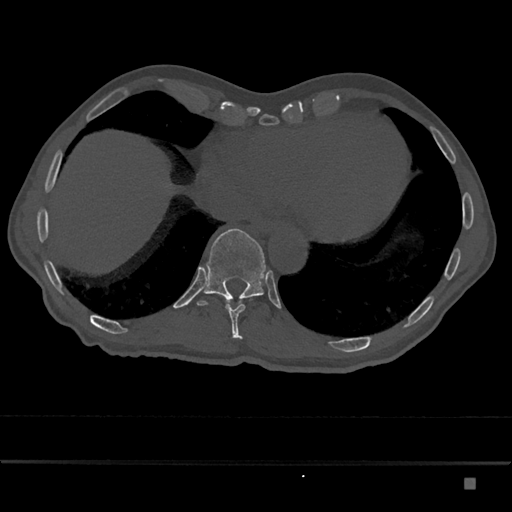
CT including the spine, one axial slice; slice 708 of 797 in the series (ordered by position); reconstruction kernel Br40s/3; bone window (W 1800 / L 400 HU); 0.5 mm slice thickness; 512 × 512 image matrix, field of view 390 × 390 mm. Male patient, age 72 years. Case-level facts recorded for this patient, not image findings: primary cancer: prostate.
Structures marked on this image (semi-automatic segmentation, software-assisted and operator-edited):
- T10 vertebra: bounding box <226,296,252,339> (left, top, right, bottom; pixels)
- T11 vertebra: <197,228,266,306>